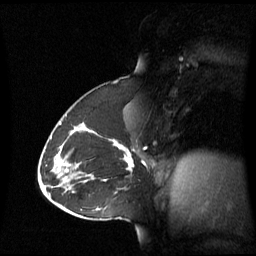
Breast MRI (dynamic contrast-enhanced), one sagittal slice. Position 37 of 60 along the scan axis. Dynamic contrast-enhanced series, image 2 of 3 at this slice position (ordered by acquisition). 1.5 T. TE 4.2 ms, TR 8.4 ms. 2.8 mm slice thickness. 256 × 256 image matrix, field of view 270 × 270 mm. Female patient, age 43 years. From the clinical record (not read from this slice): setting: breast cancer imaged before/during neoadjuvant chemotherapy; receptor status: triple-negative.
Outlined on this slice (semi-automatically segmented with operator editing):
- analysis volume of interest (the breast-tissue region the enhancement analysis was run in; not a lesion): bounding box [x1, y1, x2, y2] px = [62, 124, 137, 180]
- tumour enhancement mask (voxels above the 70 % enhancement threshold inside the analysis volume of interest): [92, 132, 134, 170]